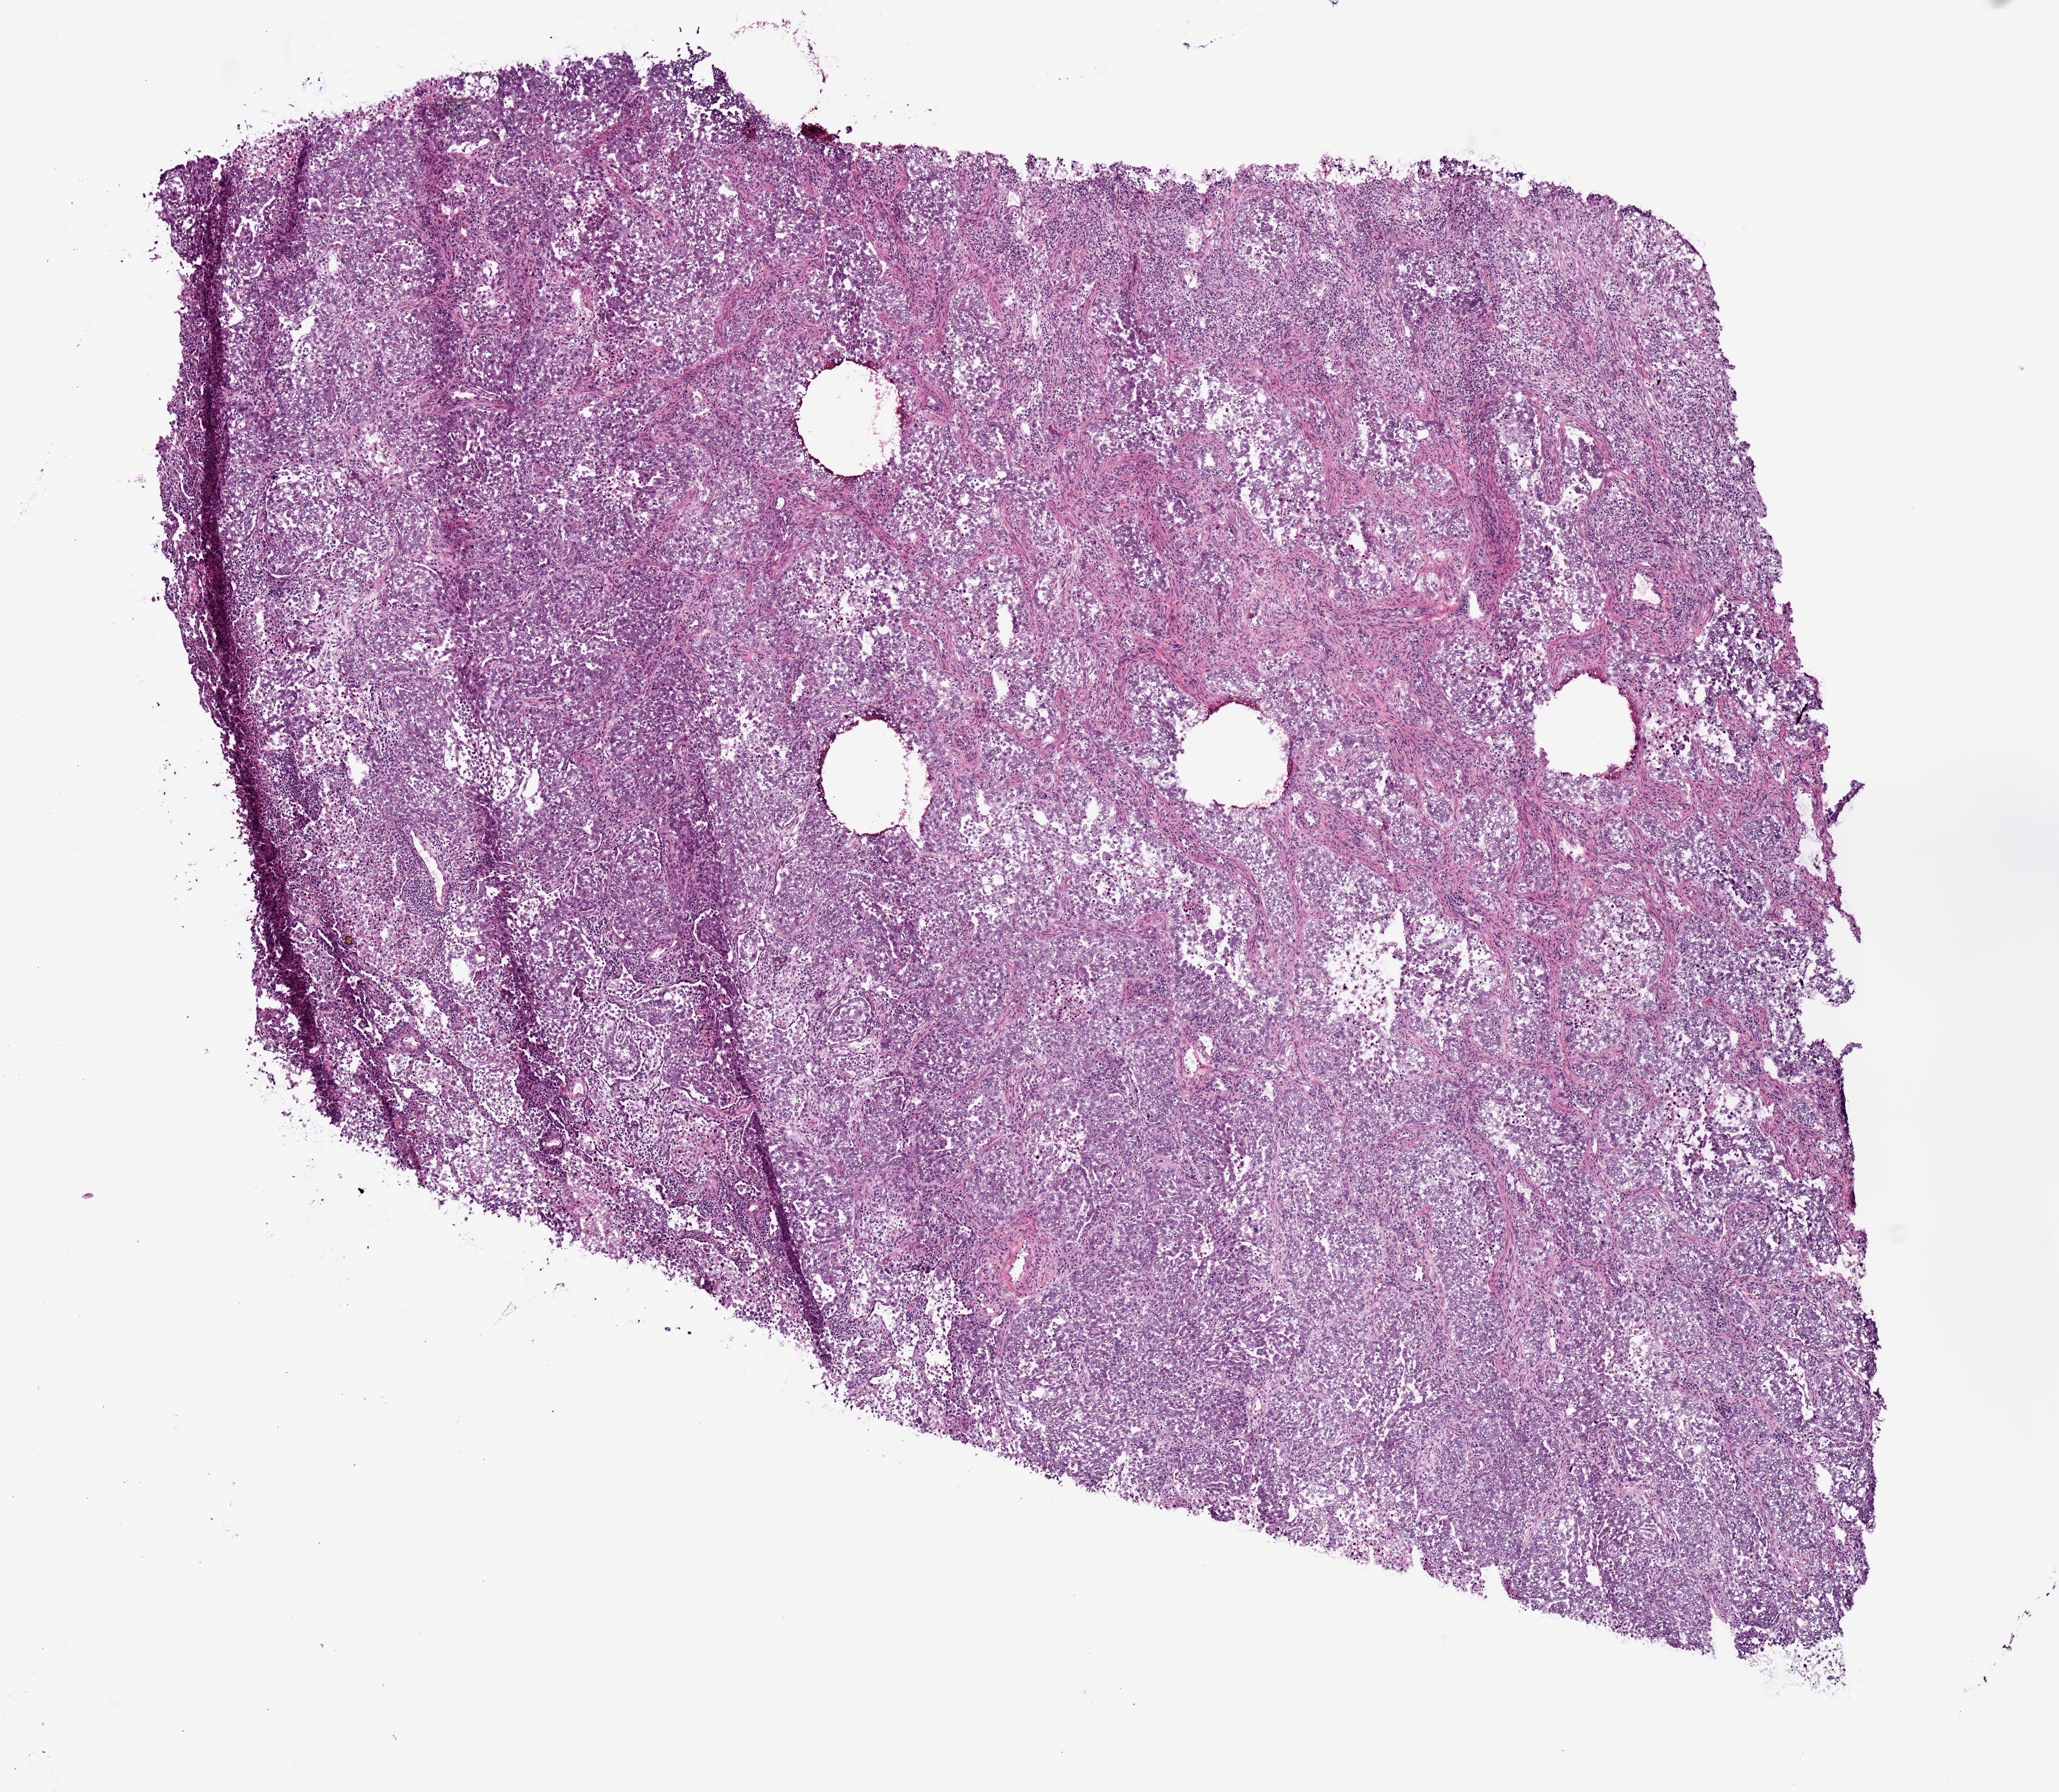
H&E-stained whole-slide image — whole scanned area (about 6.9 x 6.0 mm) shown as a low-resolution overview; frozen section from the top of the tissue portion; primary tumour sample from the lung. Male patient; age at initial diagnosis 81 years. Pathologist review of this section (percent, as recorded): tumour cells 85%, tumour nuclei 70%.
Histologic diagnosis: Adenocarcinoma, NOS.